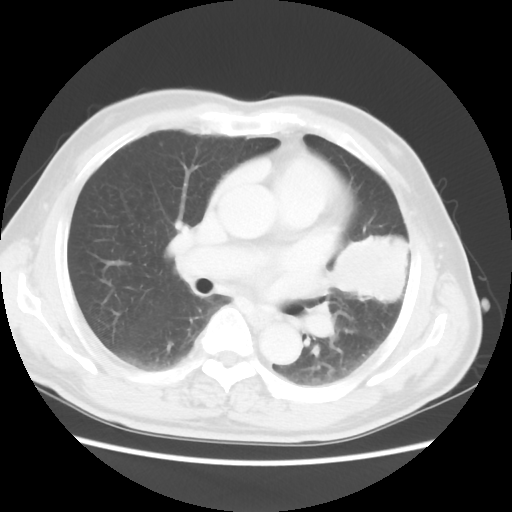
Chest CT, one axial slice. Reconstruction kernel STANDARD. 120 kVp. Lung window (W 1500 / L -600 HU). 512 × 512 image matrix, field of view 360 × 360 mm. Patient: male, 69 years. From the clinical record (not read from this slice): clinical TNM (as recorded): T3 N1 M1a.
Annotated regions visible in this slice (rectangle marked by the reading radiologist):
- lung tumour (recorded histology: squamous cell carcinoma): bounding box <329,234,419,309> (left, top, right, bottom; pixels)